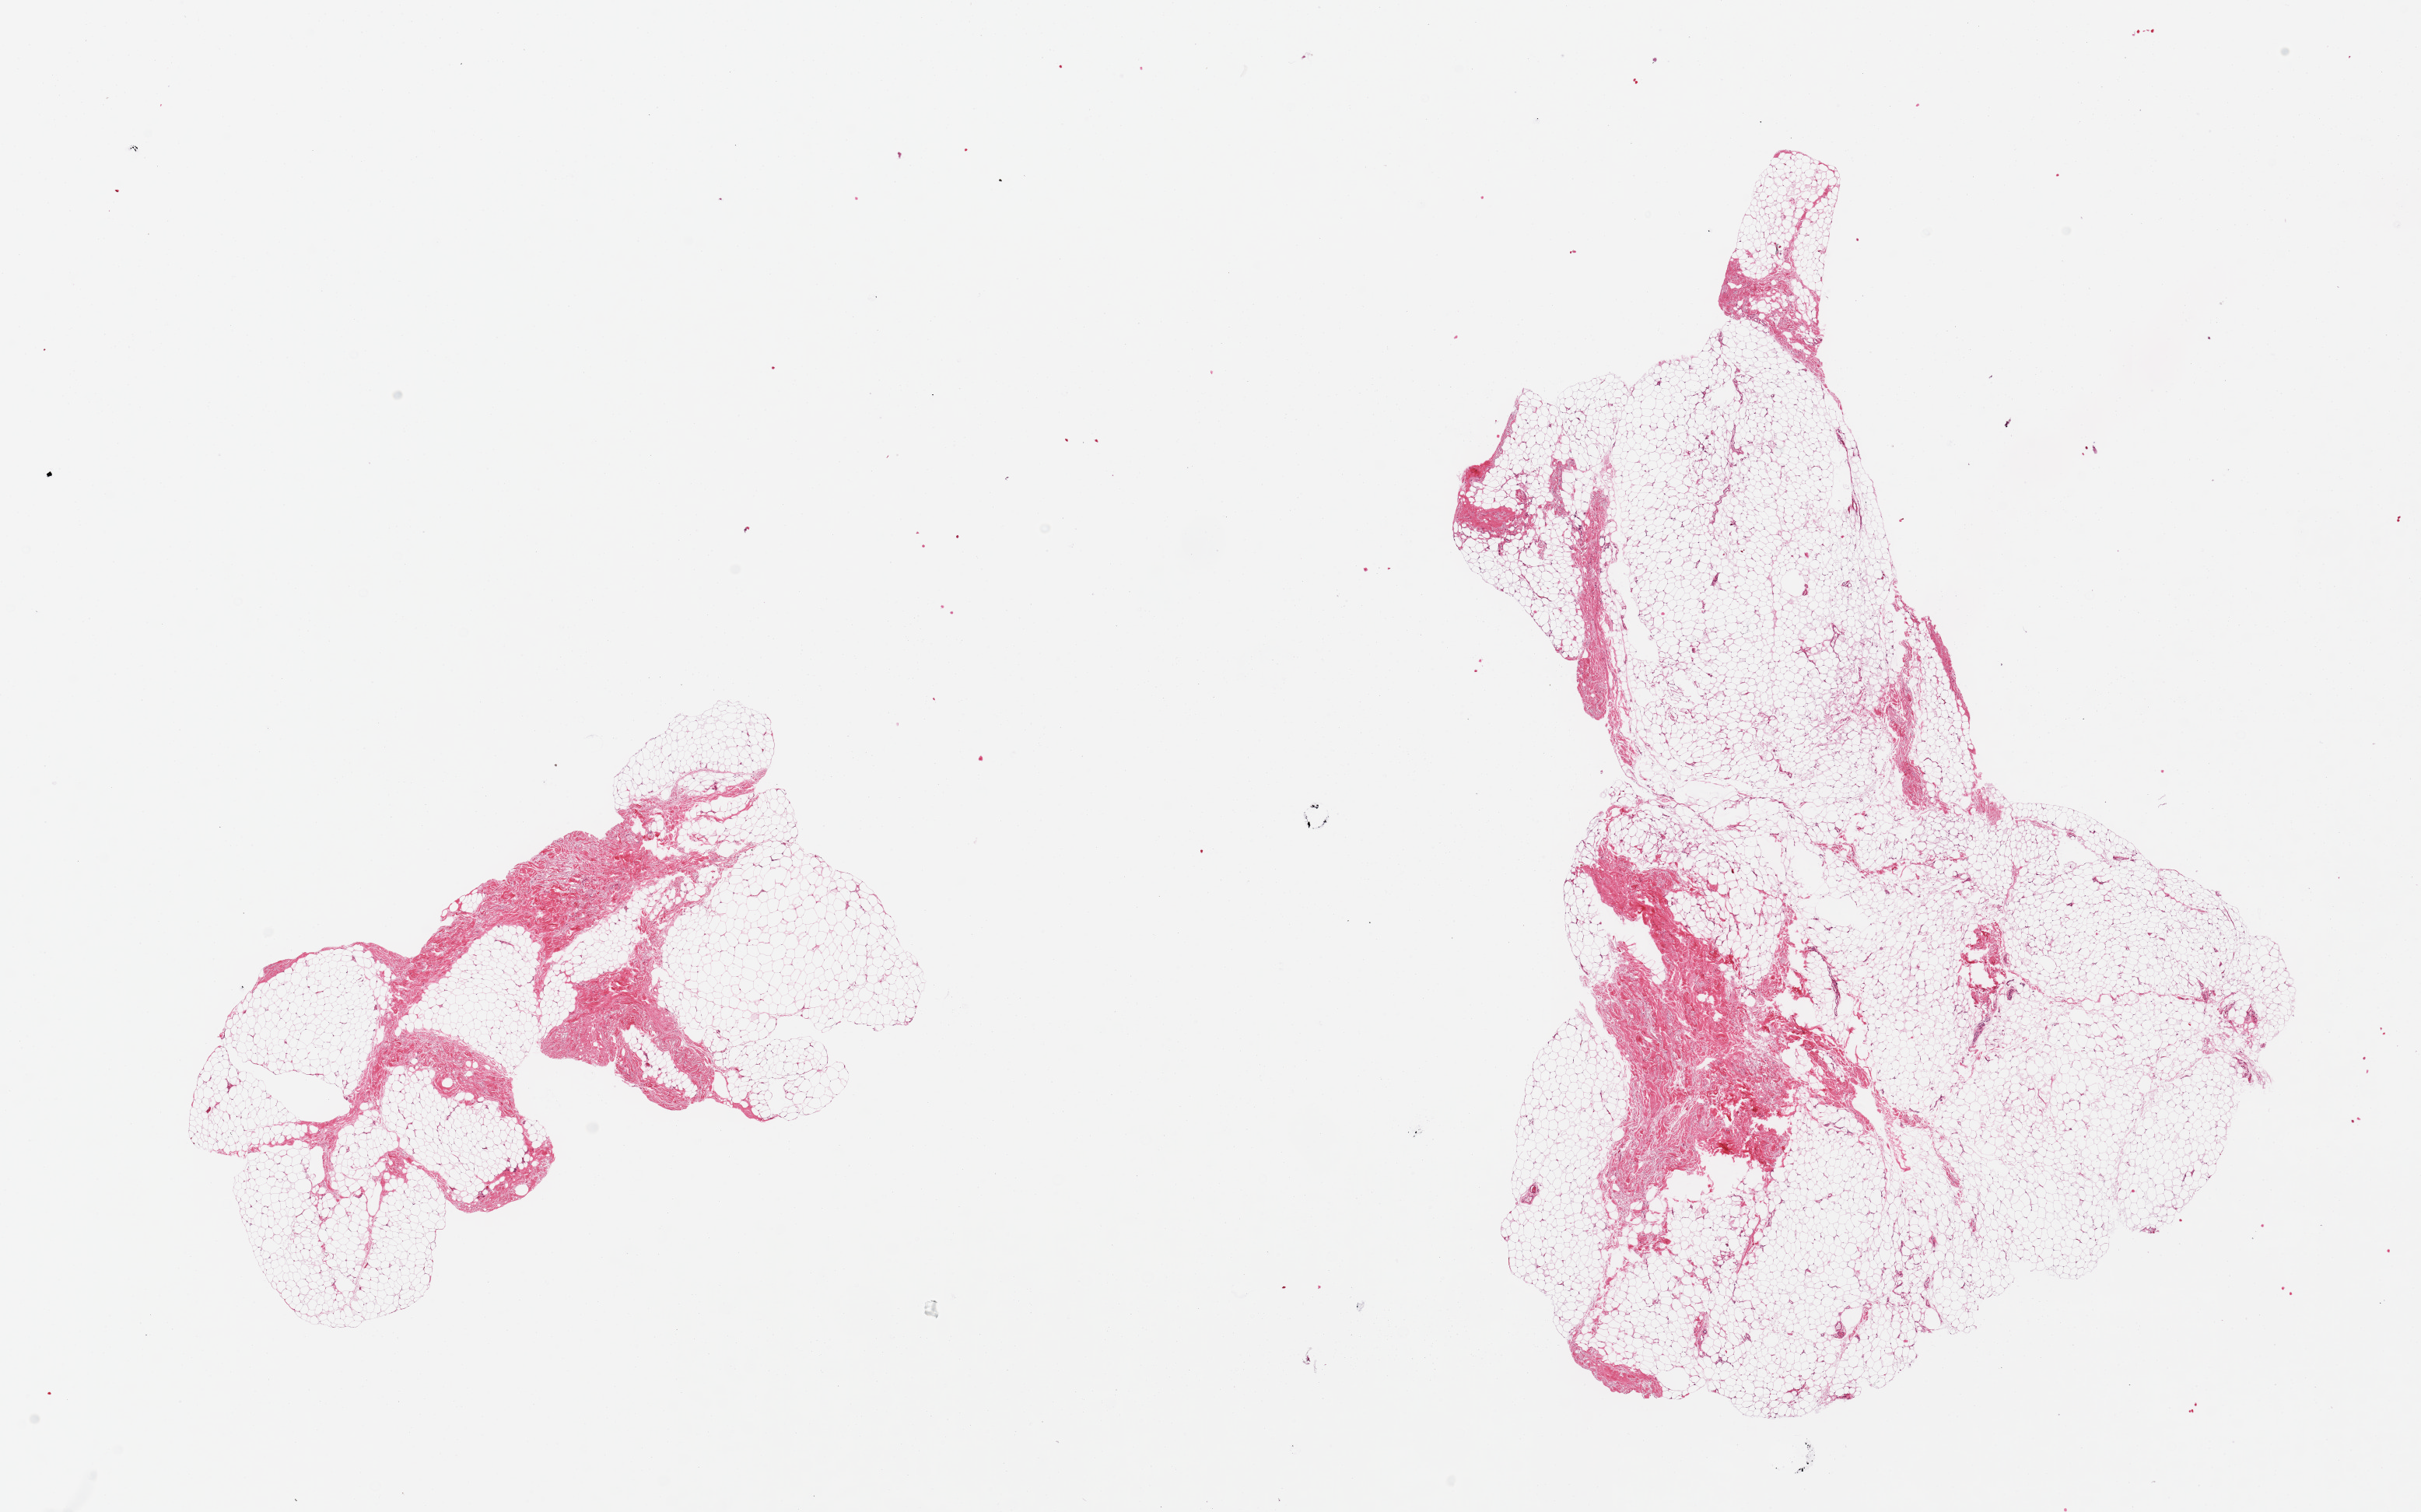
H&E whole-slide image, shown as a low-resolution overview of the whole scanned area (about 24.6 x 15.4 mm, slide scanned at 20x); PAXgene-fixed, paraffin-embedded tissue; target tissue: breast; tissue donor sample. Donor sex: male.
Reviewer comment on this tissue sample: 2 pieces, fibroadipose elements only.